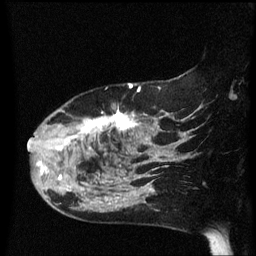
Breast MRI (dynamic contrast-enhanced), one sagittal slice; position 45 of 60 along the scan axis; dynamic contrast-enhanced series, image 2 of 3 at this slice position (ordered by acquisition); 1.5 T; TE 4.2 ms, TR 8.4 ms; 2.2 mm slice thickness; 256 × 256 image matrix, field of view 200 × 200 mm. Female patient, age 47 years.
Annotated regions visible in this slice (semi-automatically segmented with operator editing):
- analysis volume of interest (the breast-tissue region the enhancement analysis was run in; not a lesion): bounding box <28,102,149,206> (left, top, right, bottom; pixels)
- tumour enhancement mask (voxels above the 70 % enhancement threshold inside the analysis volume of interest): <28,110,141,202>